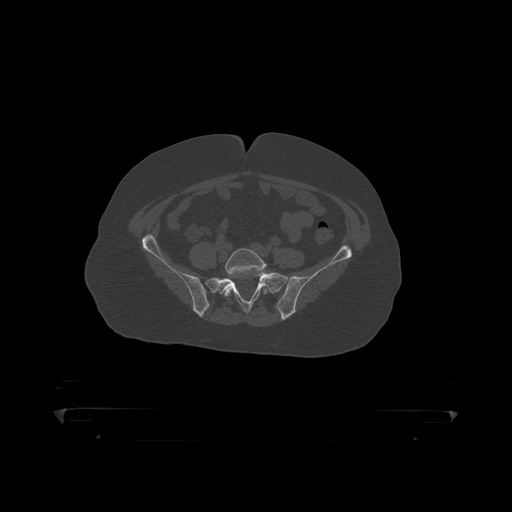
CT including the spine, one axial slice; slice 28 of 390 in the series (ordered by position); 120 kVp; bone window (W 1800 / L 400 HU); 1.25 mm slice thickness; 512 × 512 image matrix, field of view 650 × 650 mm. Male patient, age 60 years. From the clinical record (not read from this slice): primary cancer: prostate.
Annotated regions visible in this slice (semi-automatically segmented with operator editing):
- L5 vertebra: bounding box (x1, y1, x2, y2) in pixels: (224, 249, 270, 298)